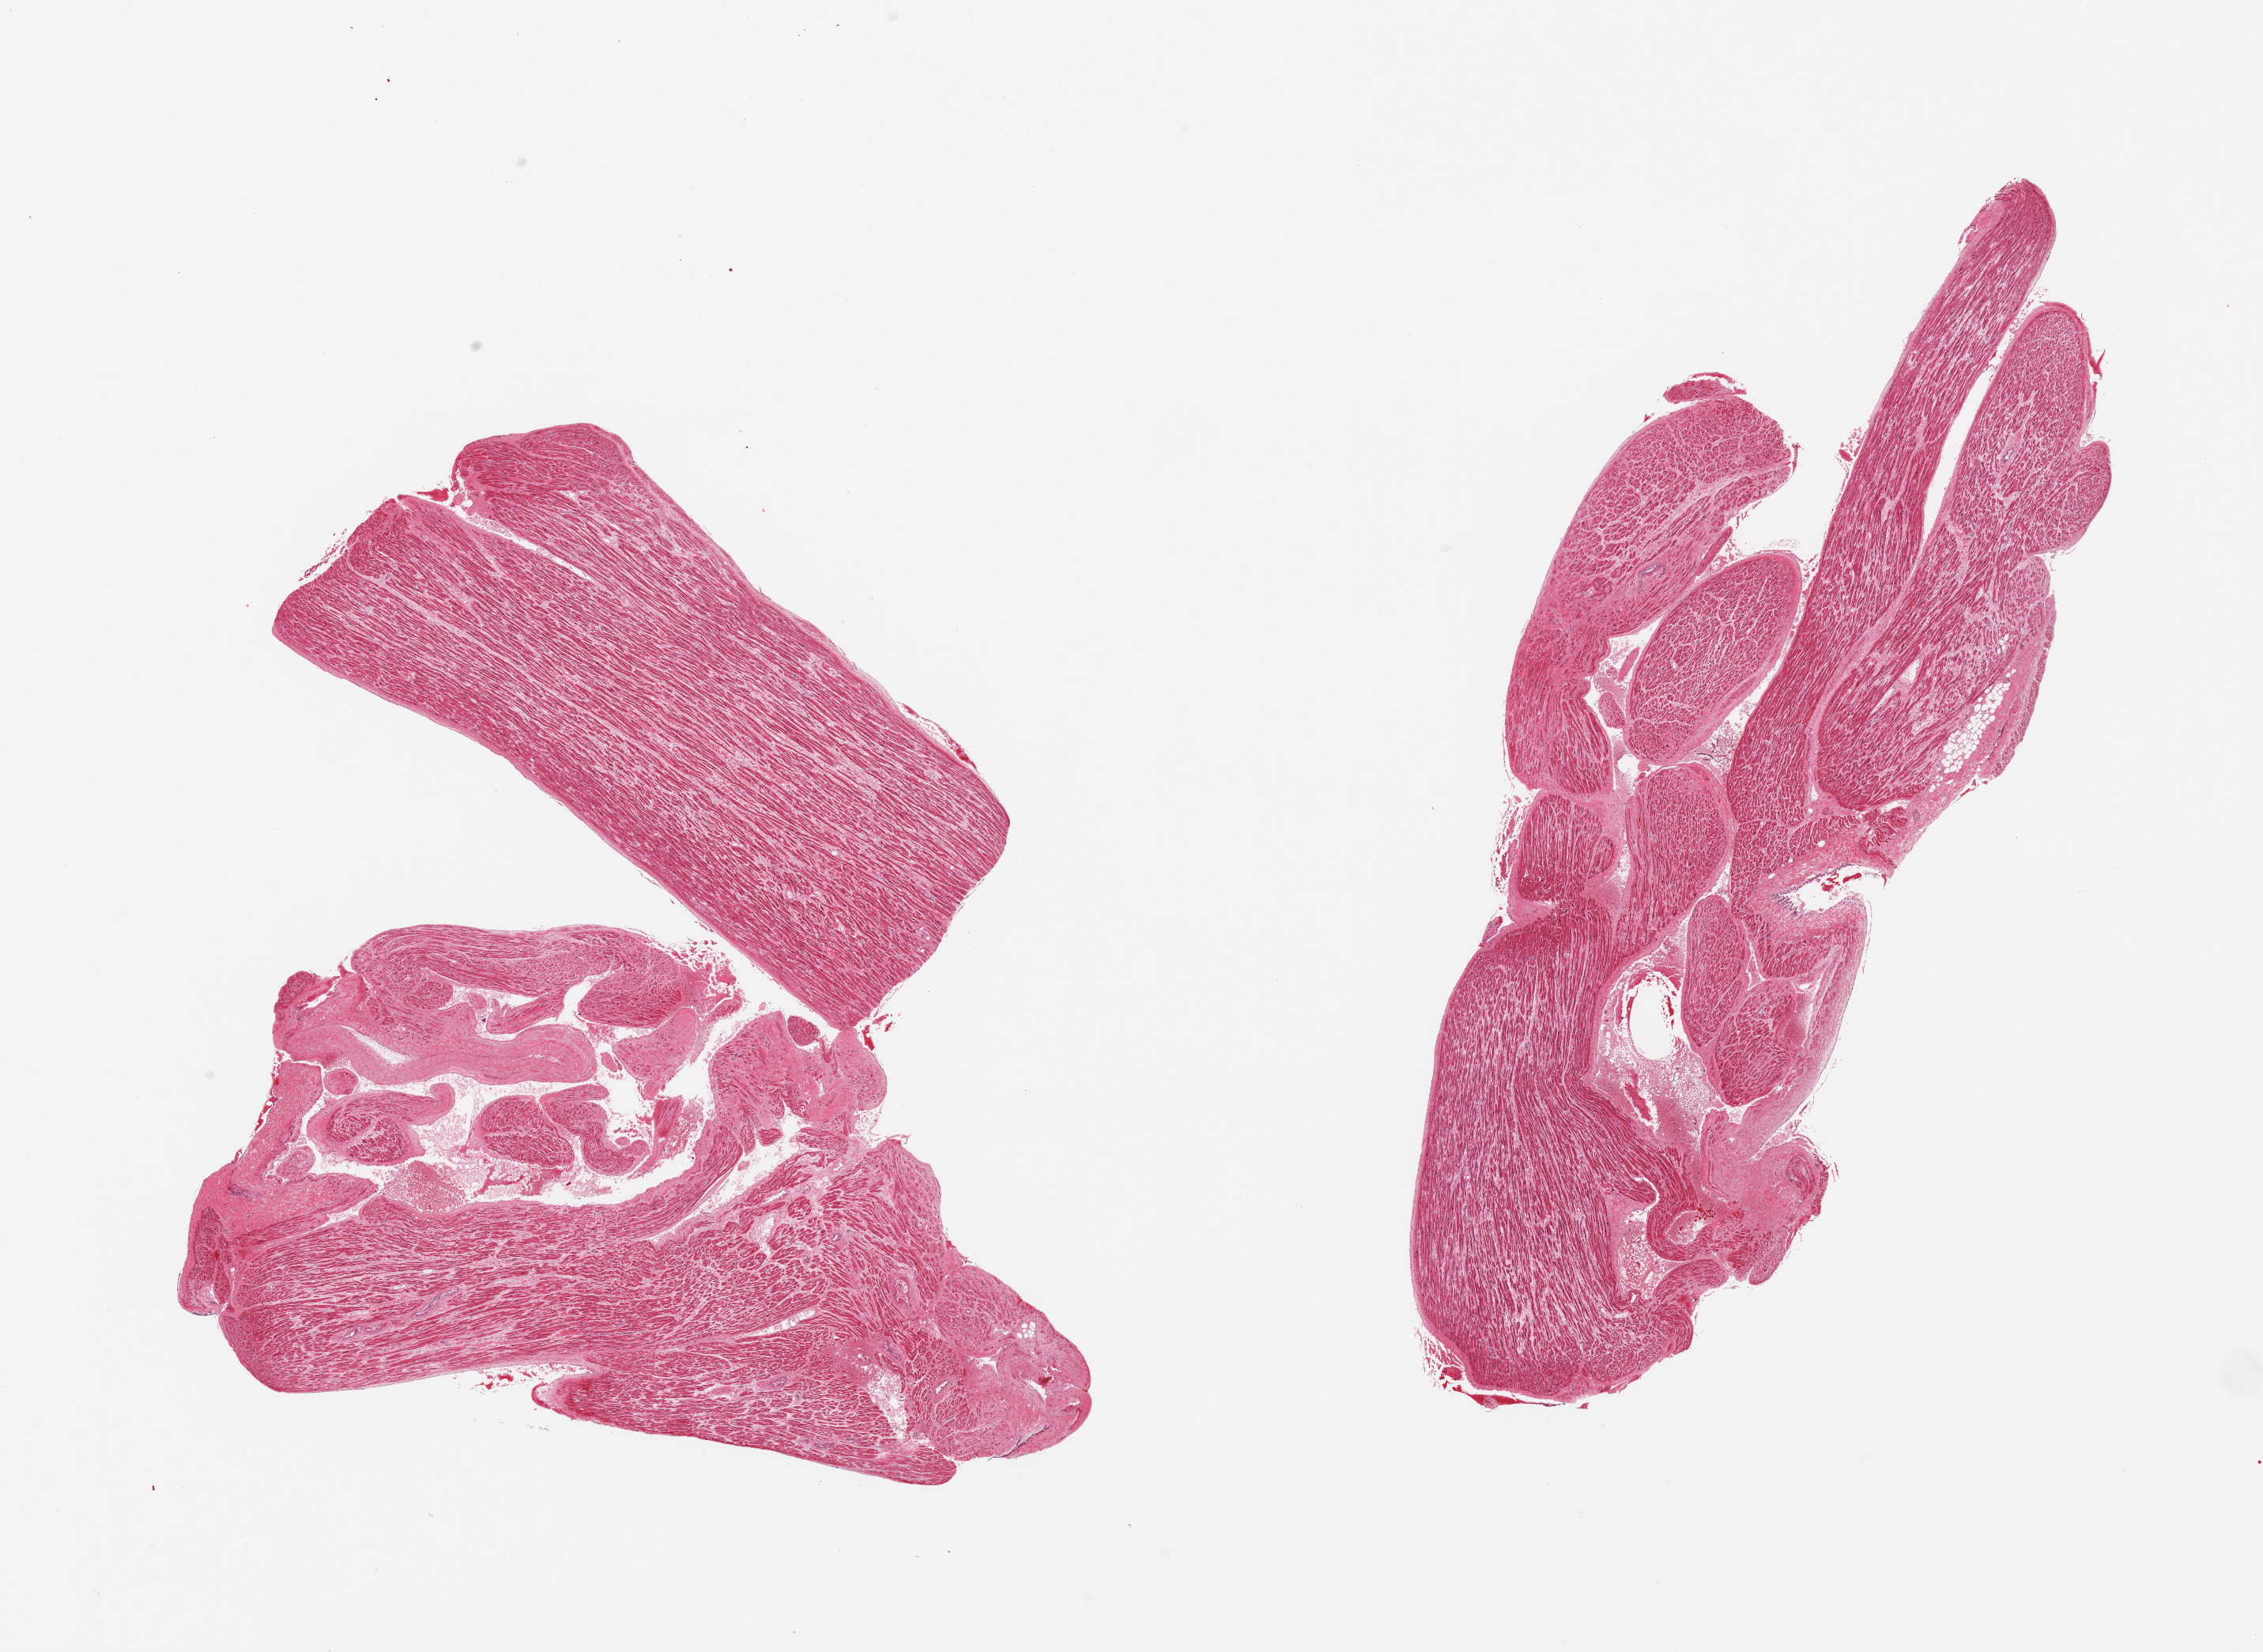
Whole-slide image, haematoxylin and eosin stain — a low-resolution overview of the entire scanned area, about 22.6 x 16.5 mm. PAXgene-fixed paraffin-embedded (PFPE) section. Section of auricular appendage (target tissue). Donor tissue sample. Donor: male.
- reviewer comment on this tissue sample: 2 pieces; some interstitial fibrosis